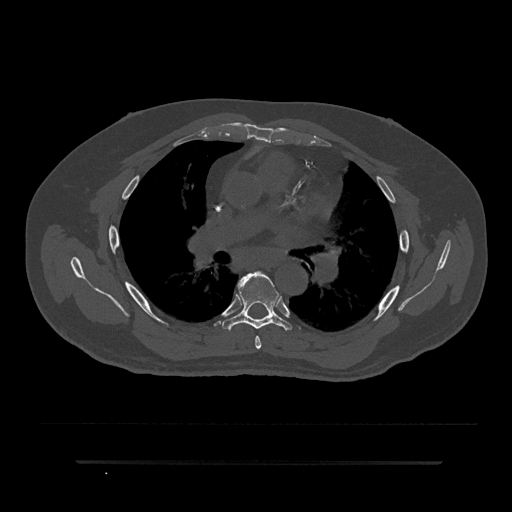
CT including the spine, one axial slice; slice 536 of 797 in the series (ordered by position); reconstruction kernel Br40s/3; 120 kVp; bone window (W 1800 / L 400 HU); 0.5 mm slice thickness; 512 × 512 image matrix, field of view 464 × 464 mm. Male patient, age 59 years. Case-level facts recorded for this patient, not image findings: primary cancer: bile ducts; vertebrae with lytic lesions (as recorded): T10.
Annotated regions visible in this slice (semi-automatic segmentation, software-assisted and operator-edited):
- T5 vertebra: bounding box [x1, y1, x2, y2] px = [255, 274, 264, 349]
- T6 vertebra: [222, 271, 292, 331]